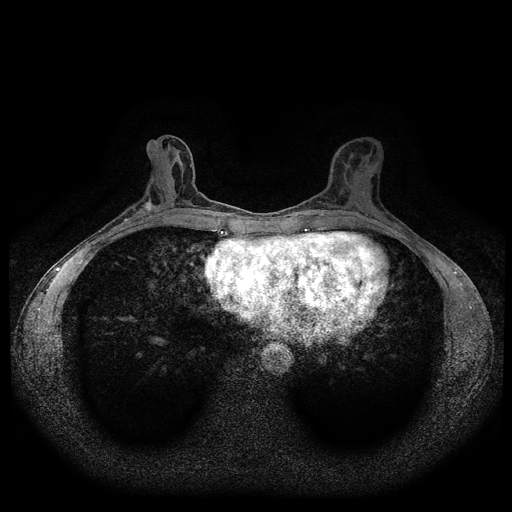
Breast MRI (dynamic contrast-enhanced, multi-phase), one axial slice; slice 44 of 116 in the series (ordered by position); dynamic contrast-enhanced series, time point 2 of 5 at this slice position (early post-contrast); 1.5 T; TE 2.6 ms, TR 5.3 ms; 2 mm slice thickness; 512 × 512 image matrix, field of view 350 × 350 mm. Female patient, age 50 years.
Structures marked on this image (semi-automatically segmented with operator editing):
- breast lesion (labelled 'tumour' in the annotation; benign lesions carry a separate 'benign' label): bounding box (x1, y1, x2, y2) in pixels: (142, 196, 154, 214)